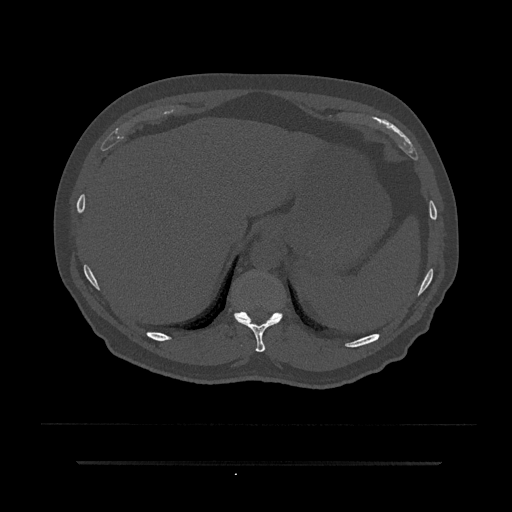
CT including the spine, one axial slice. Slice 303 of 797 in the series (ordered by position). Reconstruction kernel Br40s/3. 120 kVp. Bone window (W 1800 / L 400 HU). 0.5 mm slice thickness. 512 × 512 image matrix, field of view 464 × 464 mm. Patient: male, 59 years. Case-level facts recorded for this patient, not image findings: primary cancer: bile ducts.
Outlined on this slice (semi-automatic segmentation, software-assisted and operator-edited):
- T10 vertebra: bounding box [x1, y1, x2, y2] px = [235, 316, 282, 353]
- T11 vertebra: [234, 312, 283, 322]